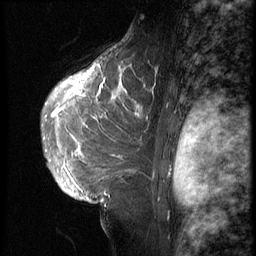
Breast MRI (dynamic contrast-enhanced), one sagittal slice. Slice 42 of 62 in the series (ordered by position). 3 images stored at this slice position (order not interpretable as contrast timing). 1.5 T. TE 4.2 ms, TR 9 ms. 256 × 256 image matrix. Female patient, age 28 years. Case-level facts recorded for this patient, not image findings: setting: breast cancer imaged before/during neoadjuvant chemotherapy.
Annotated regions visible in this slice (semi-automatic segmentation, software-assisted and operator-edited):
- analysis volume of interest (the breast-tissue region the enhancement analysis was run in; not a lesion): bounding box <42,45,158,207> (left, top, right, bottom; pixels)
- tumour enhancement mask (voxels above the 140 % enhancement threshold inside the analysis volume of interest): <51,65,157,118>